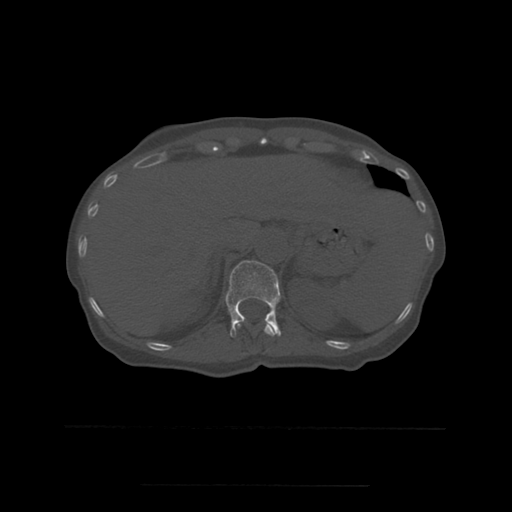
CT including the spine, one axial slice. Position 267 of 544 along the scan axis. Bone window (W 1800 / L 400 HU). 512 × 512 image matrix. Patient age 58 years. From the clinical record (not read from this slice): primary cancer: lung.
Annotated regions visible in this slice (semi-automatically segmented with operator editing):
- T11 vertebra: bounding box (x1, y1, x2, y2) in pixels: (235, 321, 277, 337)
- T12 vertebra: (226, 261, 281, 337)